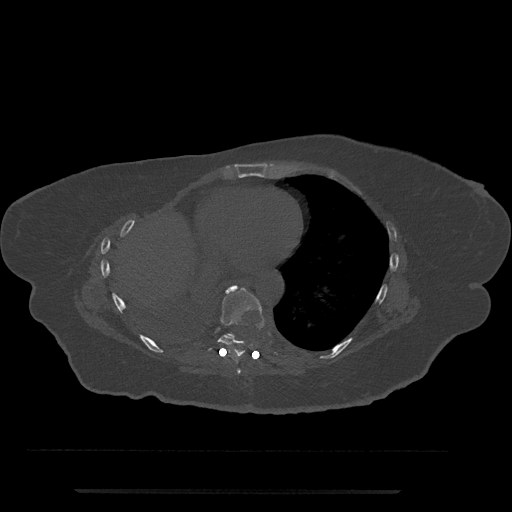
CT including the spine, one axial slice; position 383 of 797 along the scan axis; reconstruction kernel Br40s/3; 120 kVp; bone window (W 1800 / L 400 HU); 512 × 512 image matrix, field of view 440 × 440 mm. Female patient, age 51 years. Case-level facts recorded for this patient, not image findings: primary cancer: neuro.
Structures marked on this image (semi-automatic segmentation, software-assisted and operator-edited):
- T7 vertebra: bounding box (x1, y1, x2, y2) in pixels: (237, 368, 241, 374)
- T8 vertebra: (208, 285, 265, 358)
- T9 vertebra: (227, 333, 235, 340)